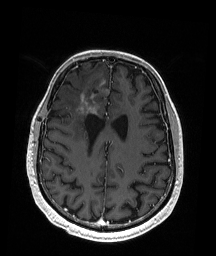
Brain MRI from a brain-tumour surgery series, one axial slice; slice 69 of 192 in the series (ordered by position); T1-weighted post-contrast; 216 × 256 image matrix, field of view 211 × 250 mm. From the clinical record (not read from this slice): histopathology: Astrocytoma; WHO grade: 3; IDH mutation: yes; tumour location: Right Frontal.
Annotated regions visible in this slice (expert manual segmentation):
- tumour: bounding box (x1, y1, x2, y2) in pixels: (81, 94, 97, 116)